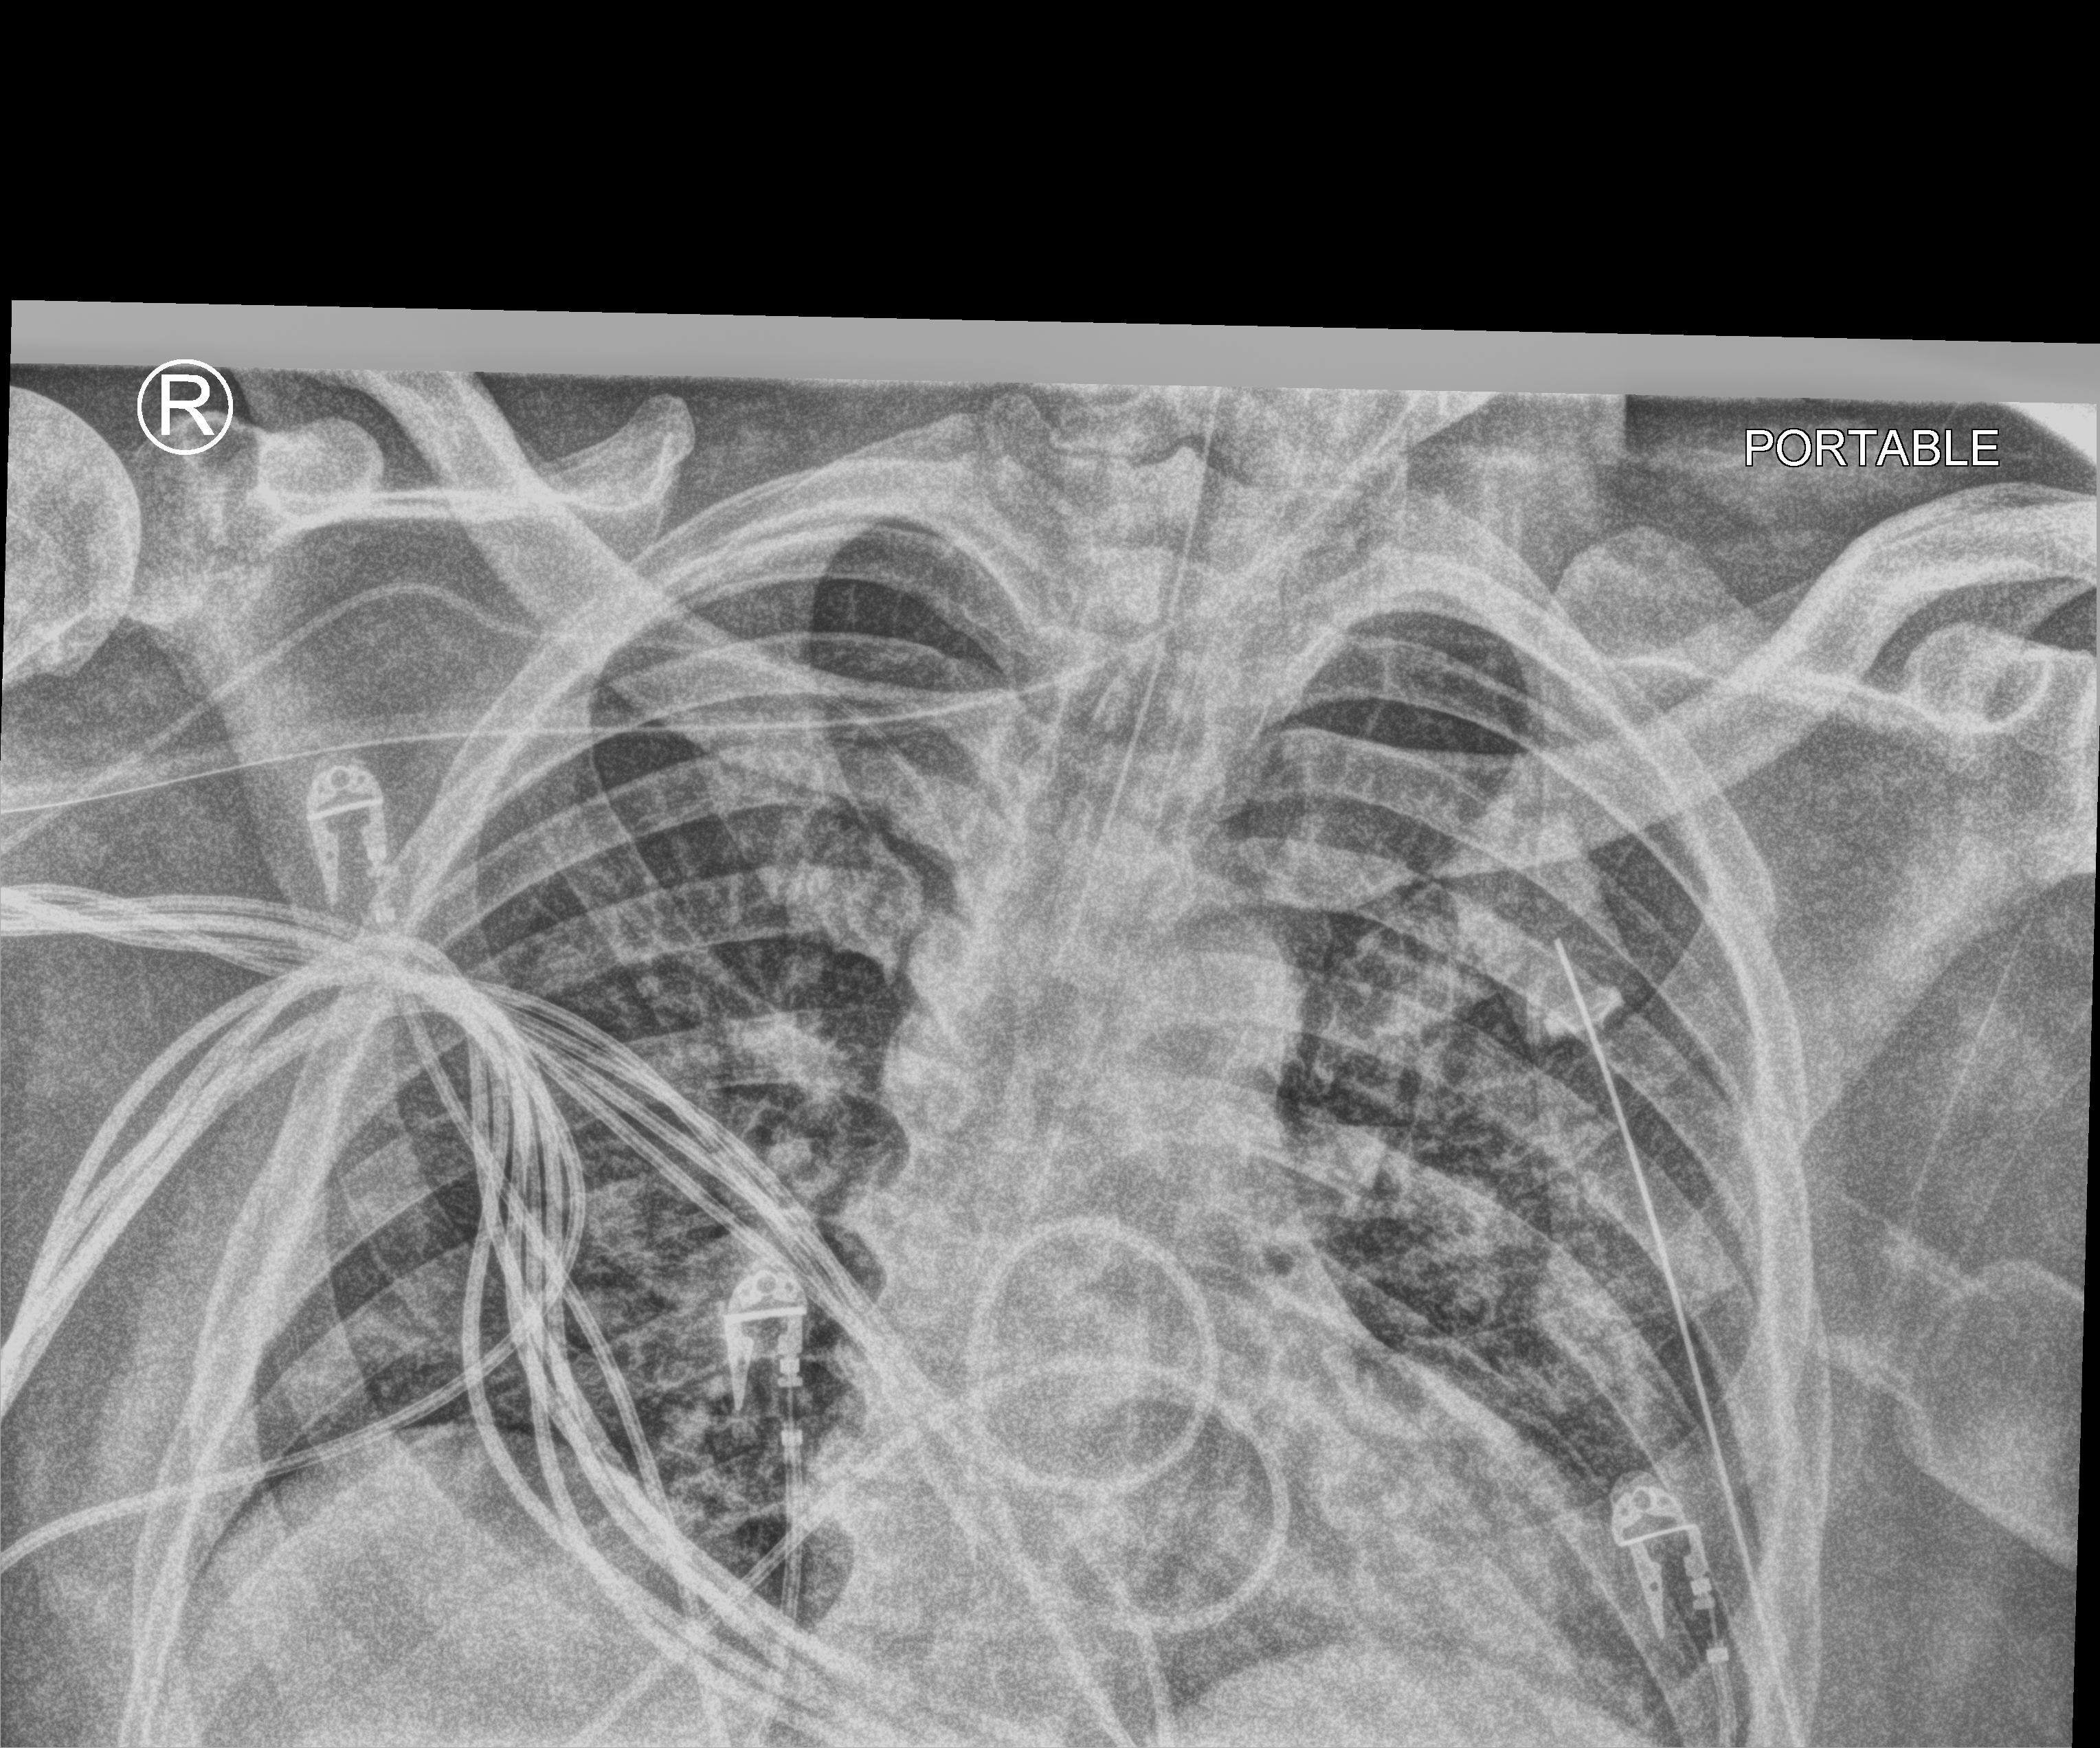
Bedside chest radiograph (computed radiography); anteroposterior (AP) projection. Patient hospitalised with COVID-19; male, aged 18–59 years.
Admission-level facts for this patient (not findings on this image; timing relative to this image not recorded):
- hypertension (admission record): no
- diabetes (admission record): no